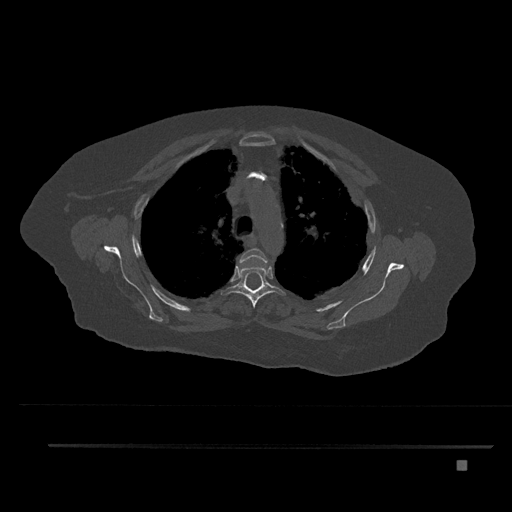
CT including the spine, one axial slice; slice 608 of 797 in the series (ordered by position); reconstruction kernel Br40s/3; 120 kVp; bone window (W 1800 / L 400 HU); 0.5 mm slice thickness; 512 × 512 image matrix, field of view 437 × 437 mm. Female patient, age 76 years. From the clinical record (not read from this slice): primary cancer: lung; vertebrae with lytic lesions (as recorded): T11, L3.
Structures marked on this image (semi-automatic segmentation, software-assisted and operator-edited):
- T3 vertebra: bounding box <240,248,268,265> (left, top, right, bottom; pixels)
- T4 vertebra: <224,257,285,308>